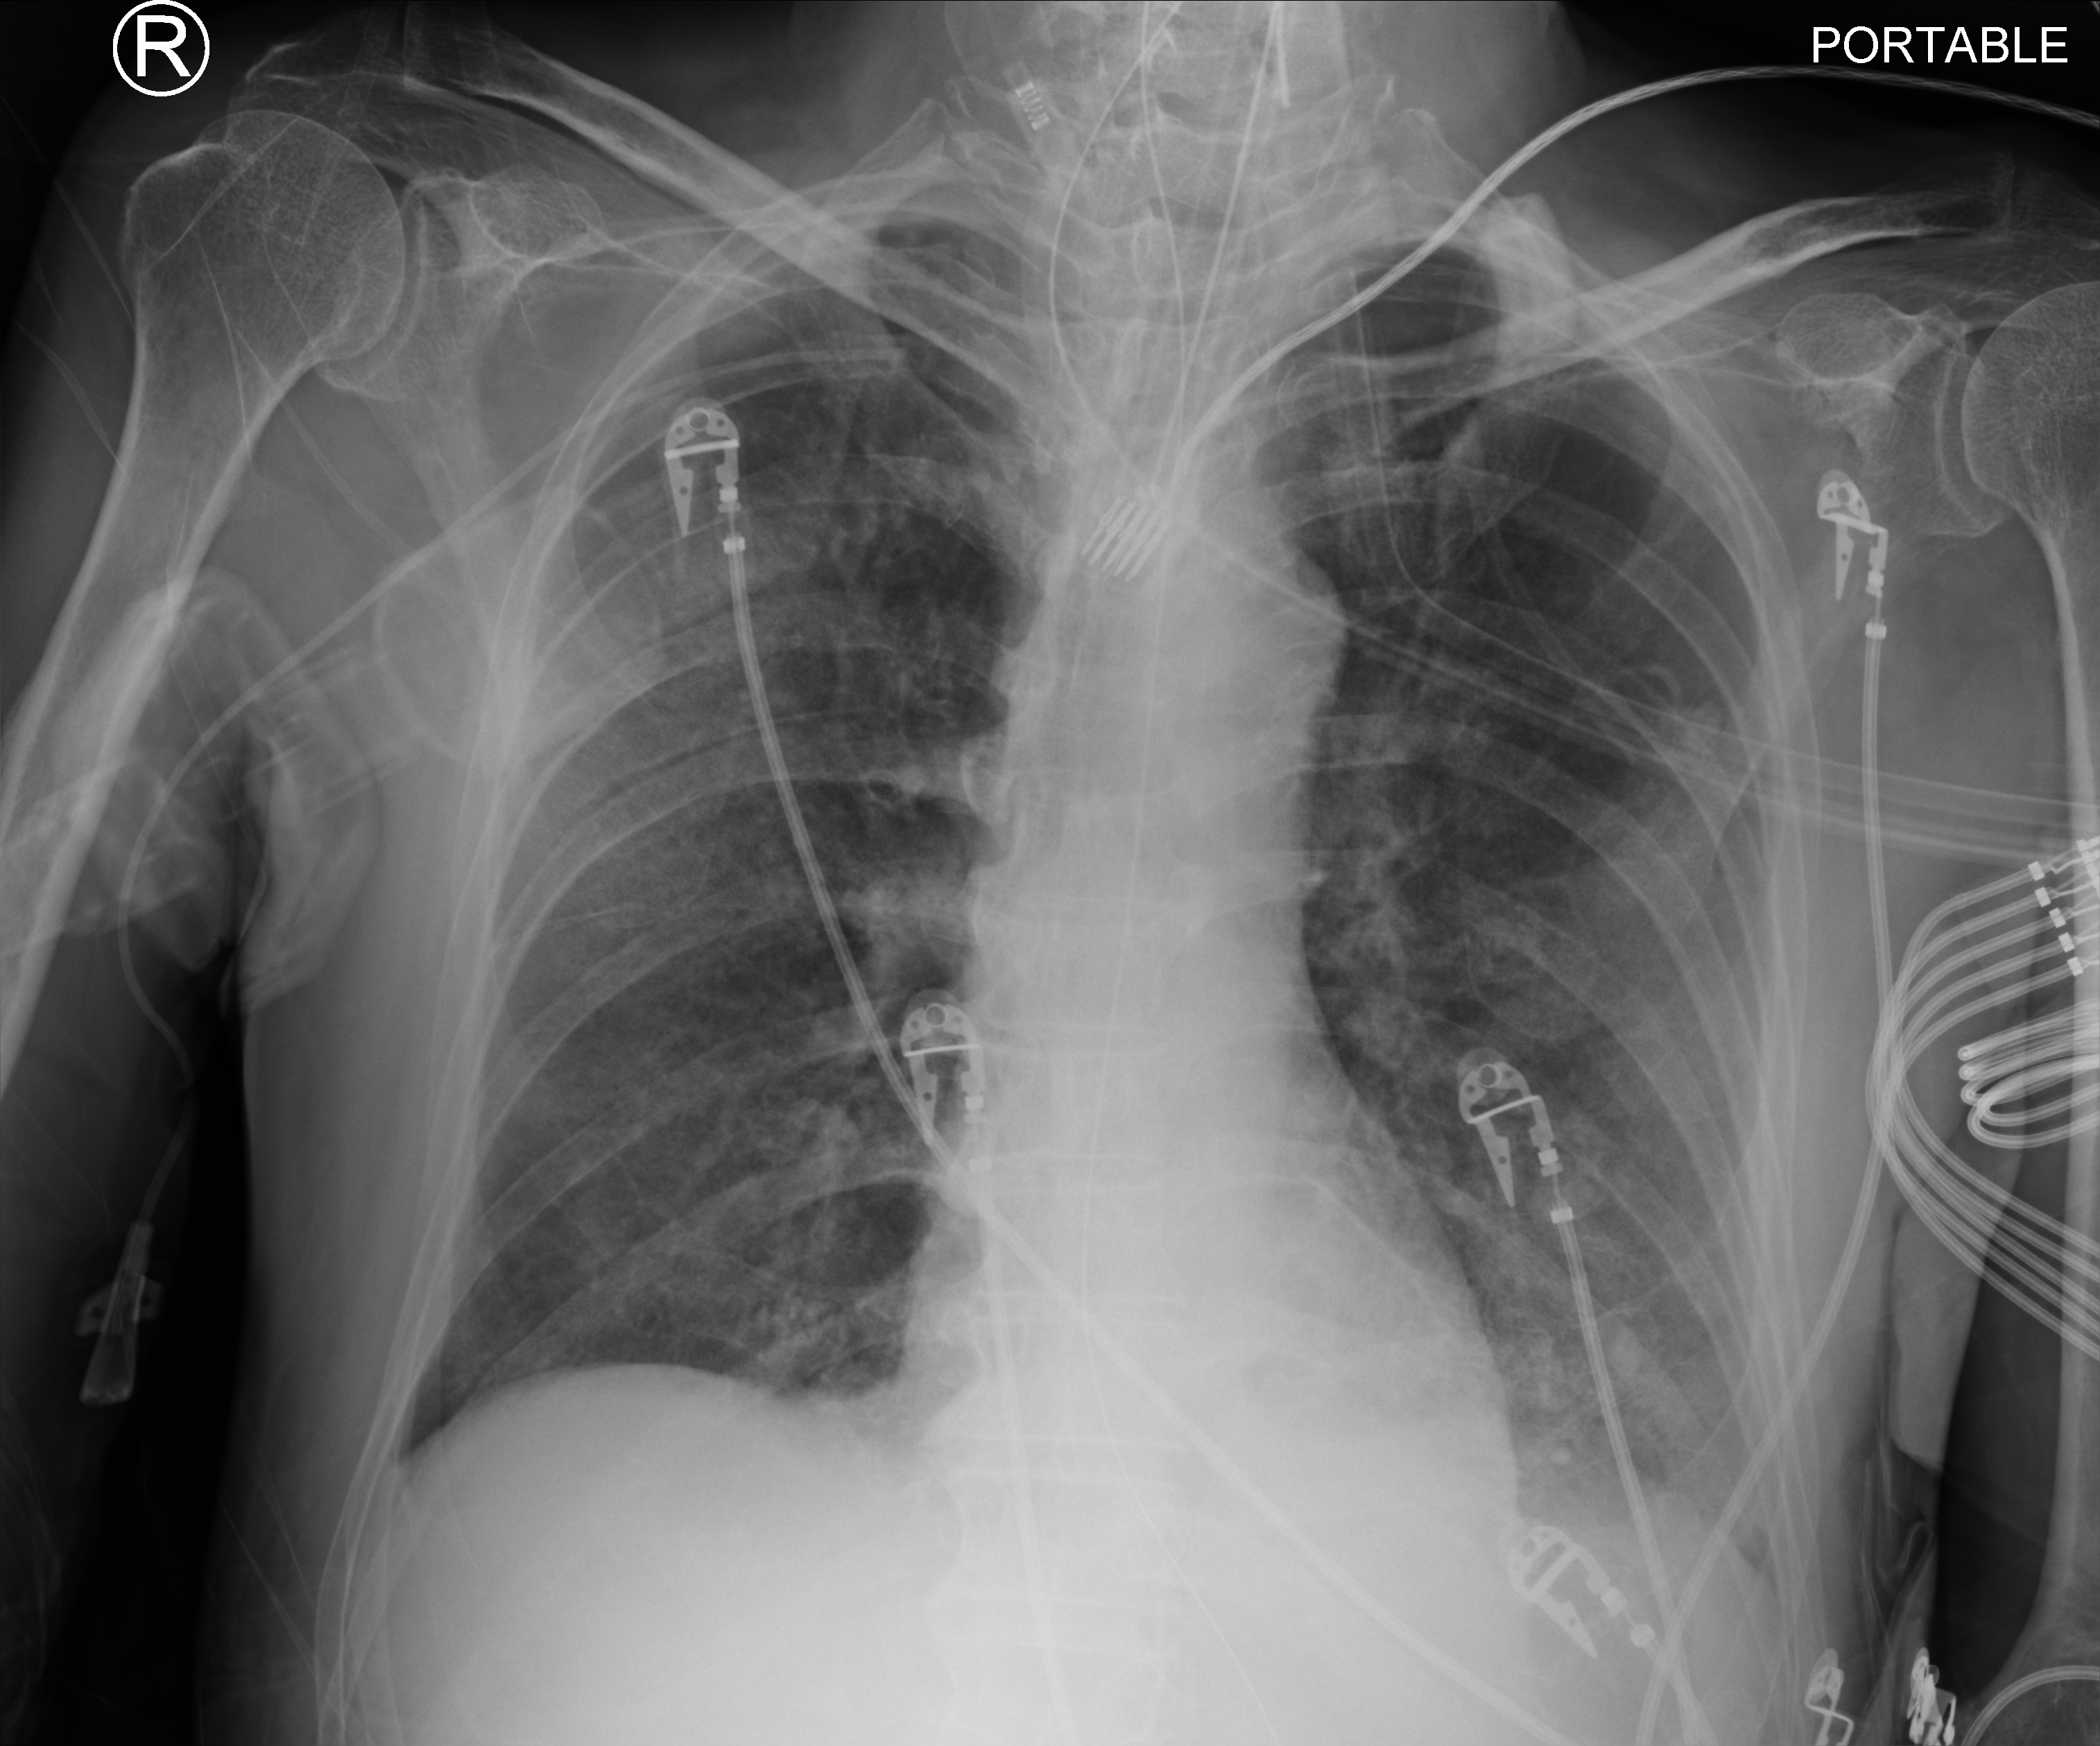
Bedside chest radiograph (computed radiography), anteroposterior (AP) projection. Patient hospitalised with COVID-19; male, aged 60–74 years.
Hospital-stay facts (about this admission, not read from this image; timing relative to this image not recorded):
- hypertension (admission record): yes
- length of hospital stay: 42 days